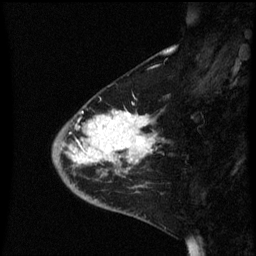
Breast MRI (dynamic contrast-enhanced), one sagittal slice. Dynamic contrast-enhanced series, image 2 of 3 at this slice position (ordered by acquisition). 1.5 T. TE 4.2 ms, TR 8.4 ms. 2.3 mm slice thickness. 256 × 256 image matrix, field of view 200 × 200 mm. Patient: female, 46 years. Case-level facts recorded for this patient, not image findings: setting: breast cancer imaged before/during neoadjuvant chemotherapy; receptor status: HER2-positive.
Annotated regions visible in this slice (semi-automatic segmentation, software-assisted and operator-edited):
- analysis volume of interest (the breast-tissue region the enhancement analysis was run in; not a lesion): bounding box <53,102,158,187> (left, top, right, bottom; pixels)
- tumour enhancement mask (voxels above the 70 % enhancement threshold inside the analysis volume of interest): <61,110,155,165>